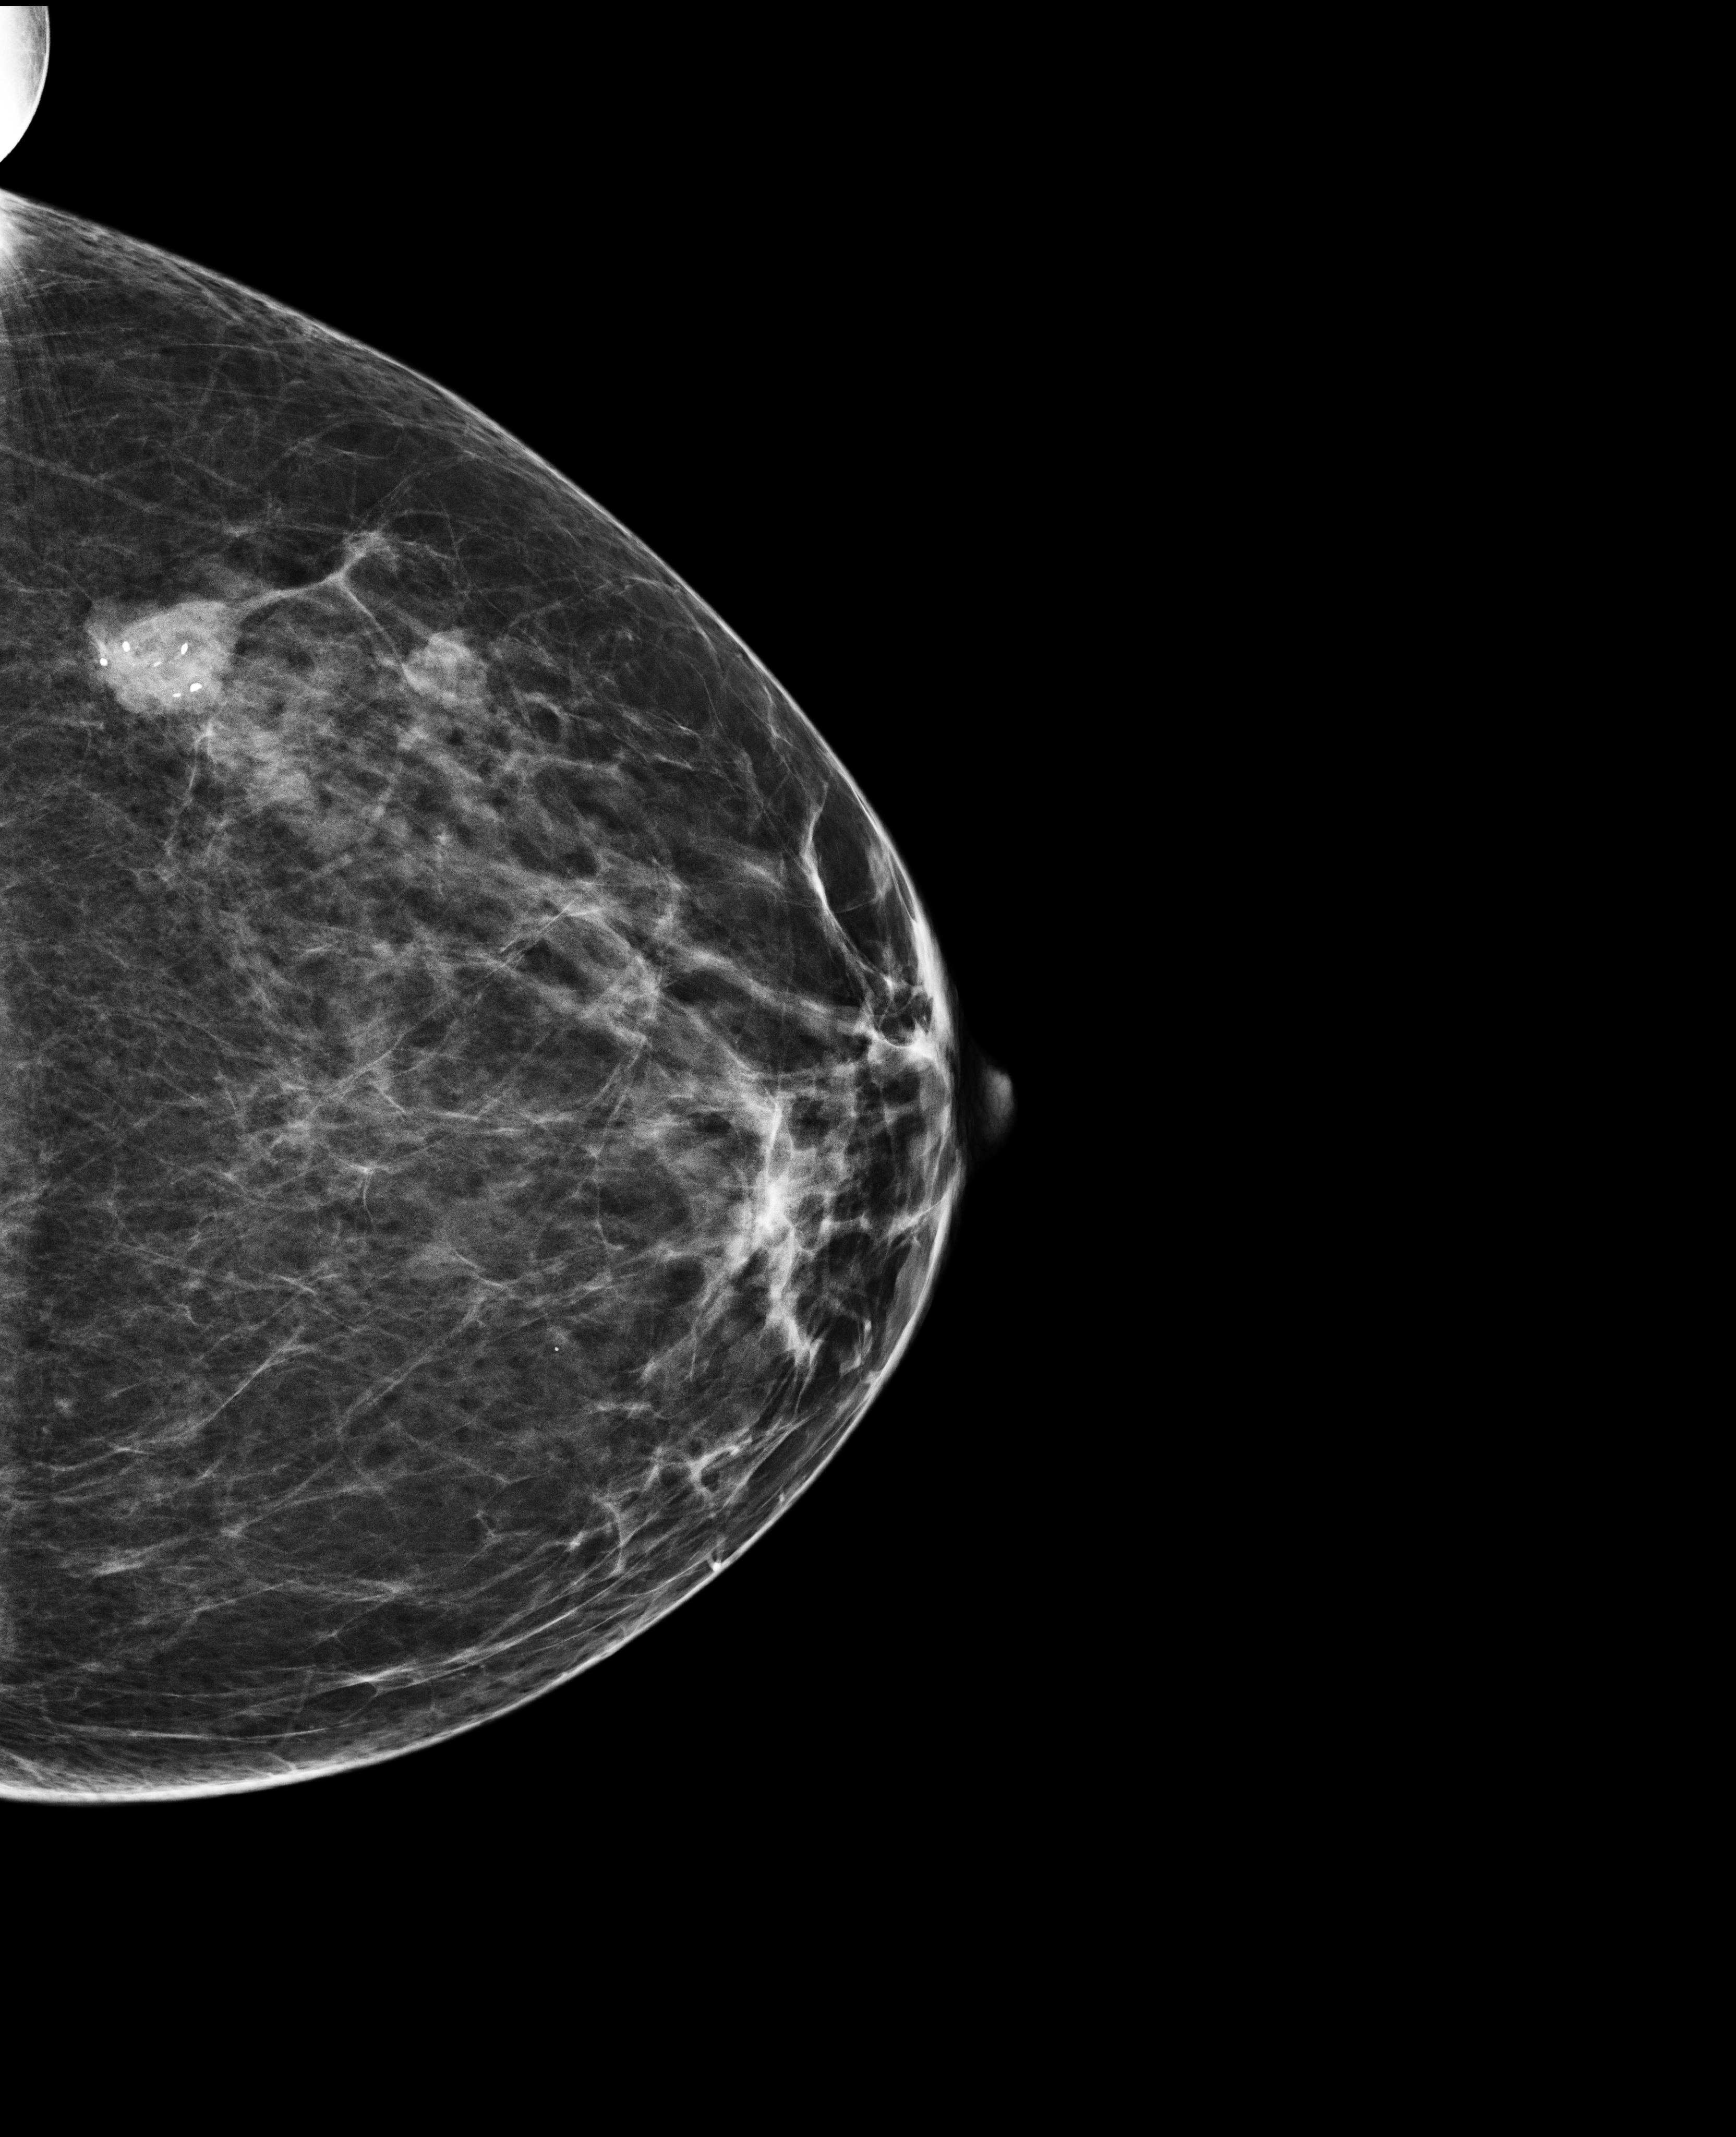
Full-field digital mammogram (FFDM), left breast, CC view, annual screening mammography examination, compressed breast thickness 54 mm. Patient: female, 64 years.
Final BI-RADS assessment for this screening round (tomosynthesis exam, both breasts): category 2.